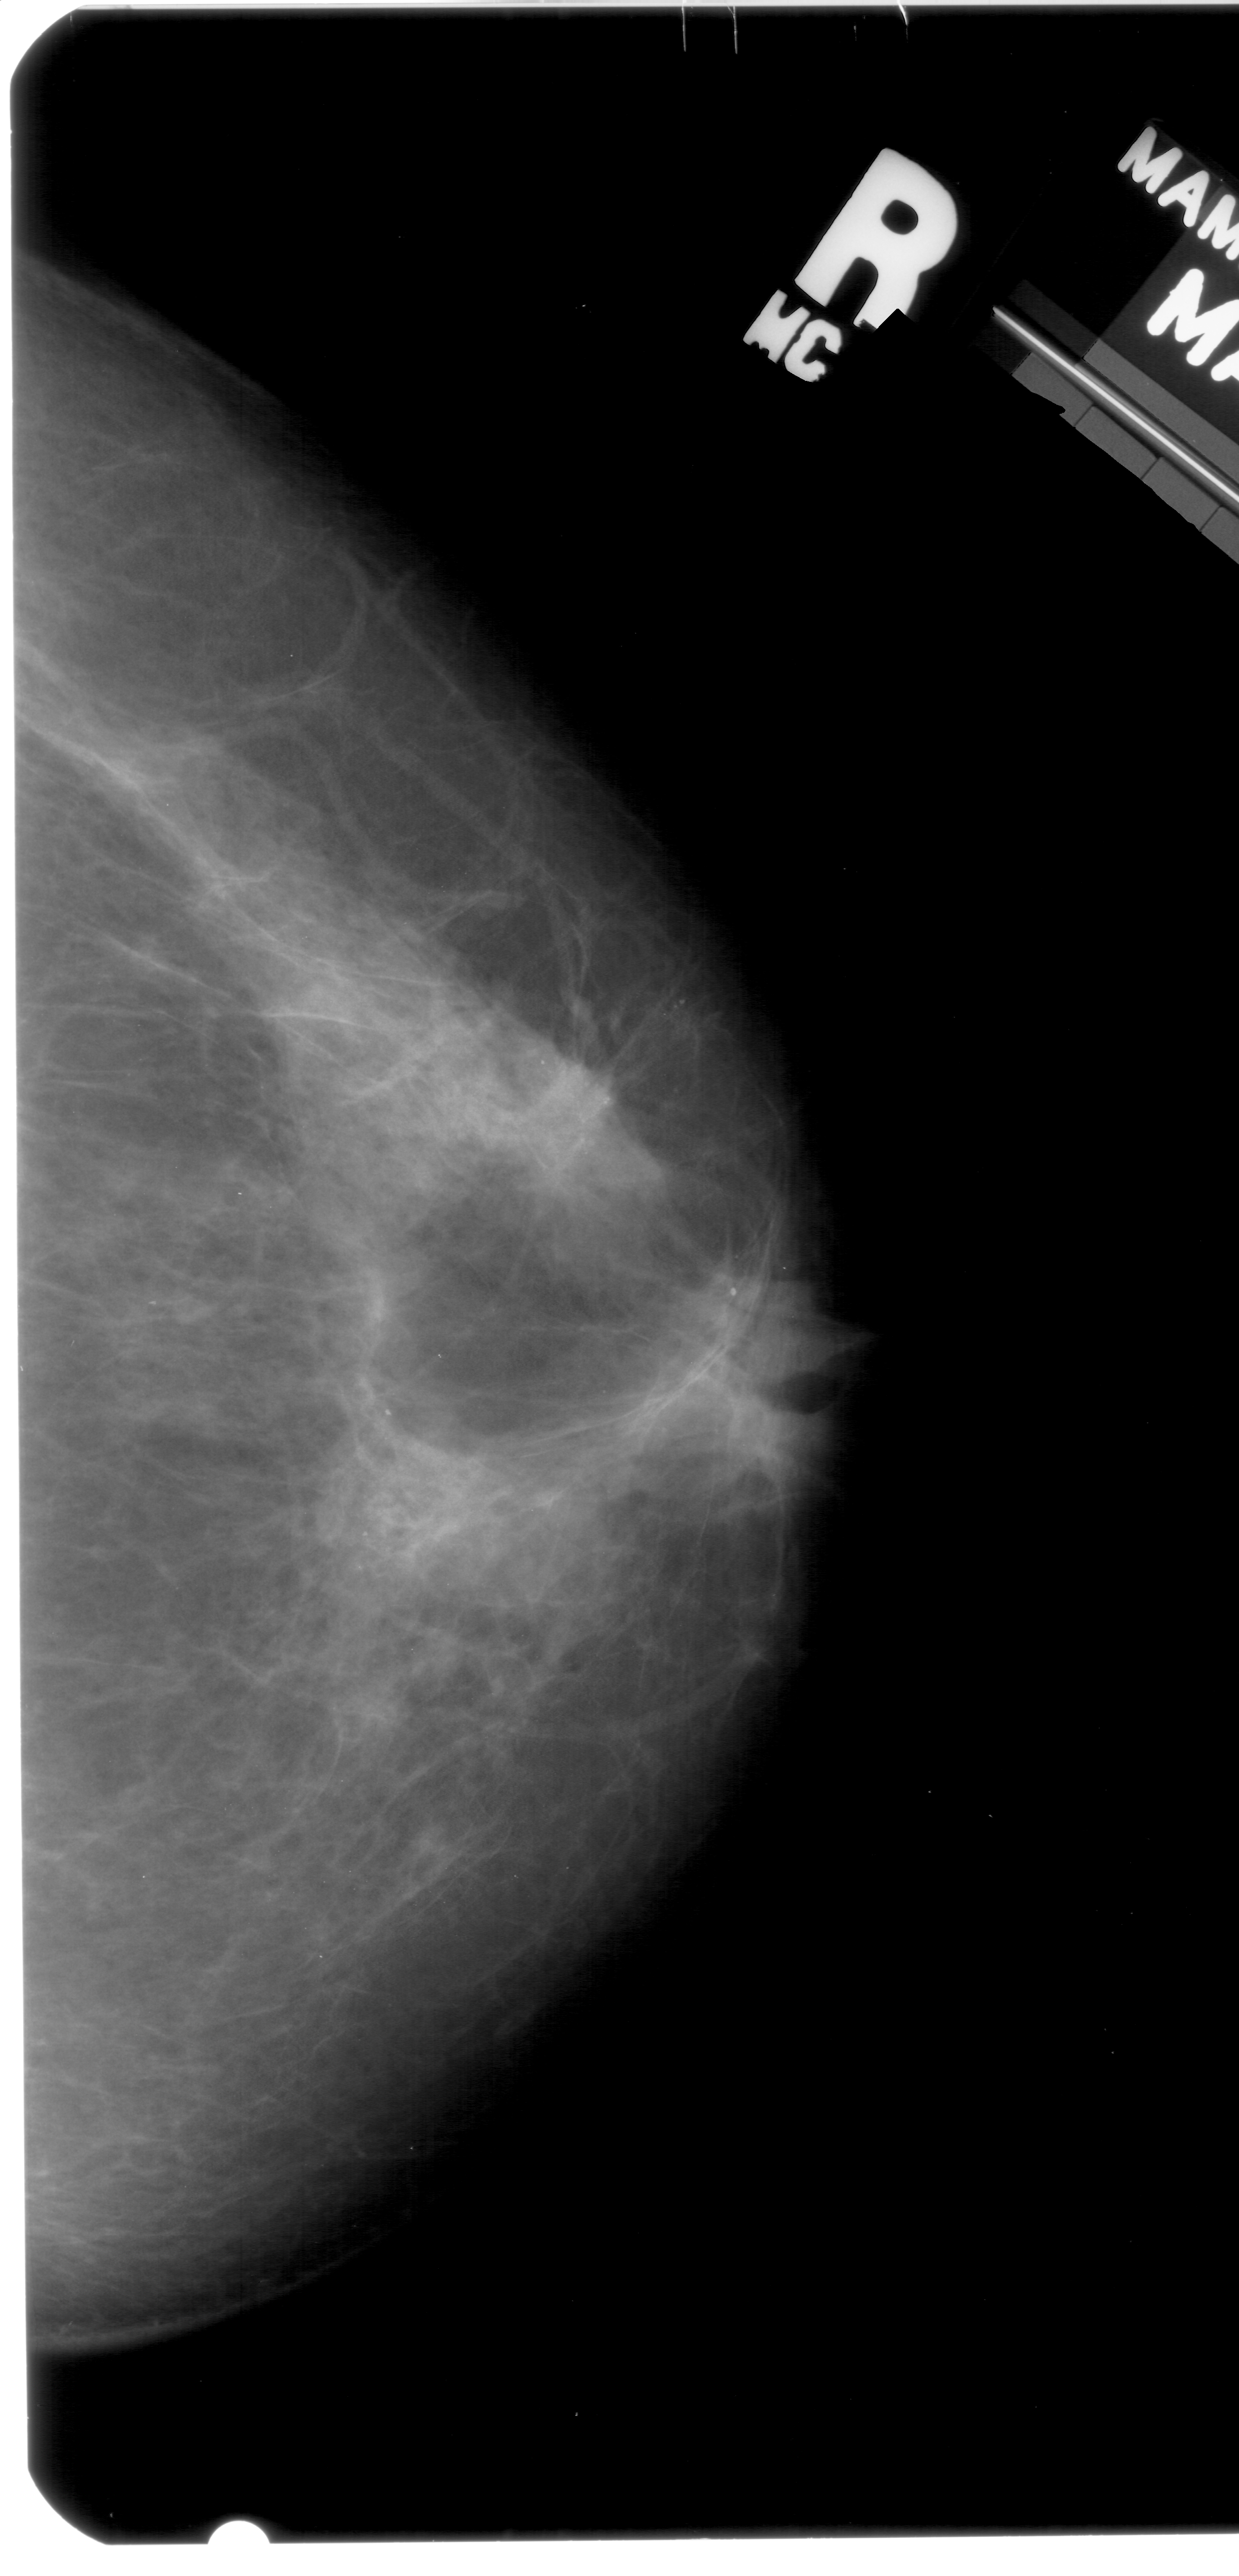
Scanned film-screen mammogram, right breast, craniocaudal (CC) view, BI-RADS breast density category 4 (scale 1–4).
- Marked abnormality: calcifications, morphology pleomorphic, distribution clustered; BI-RADS assessment category 4; pathology (as recorded): malignant.